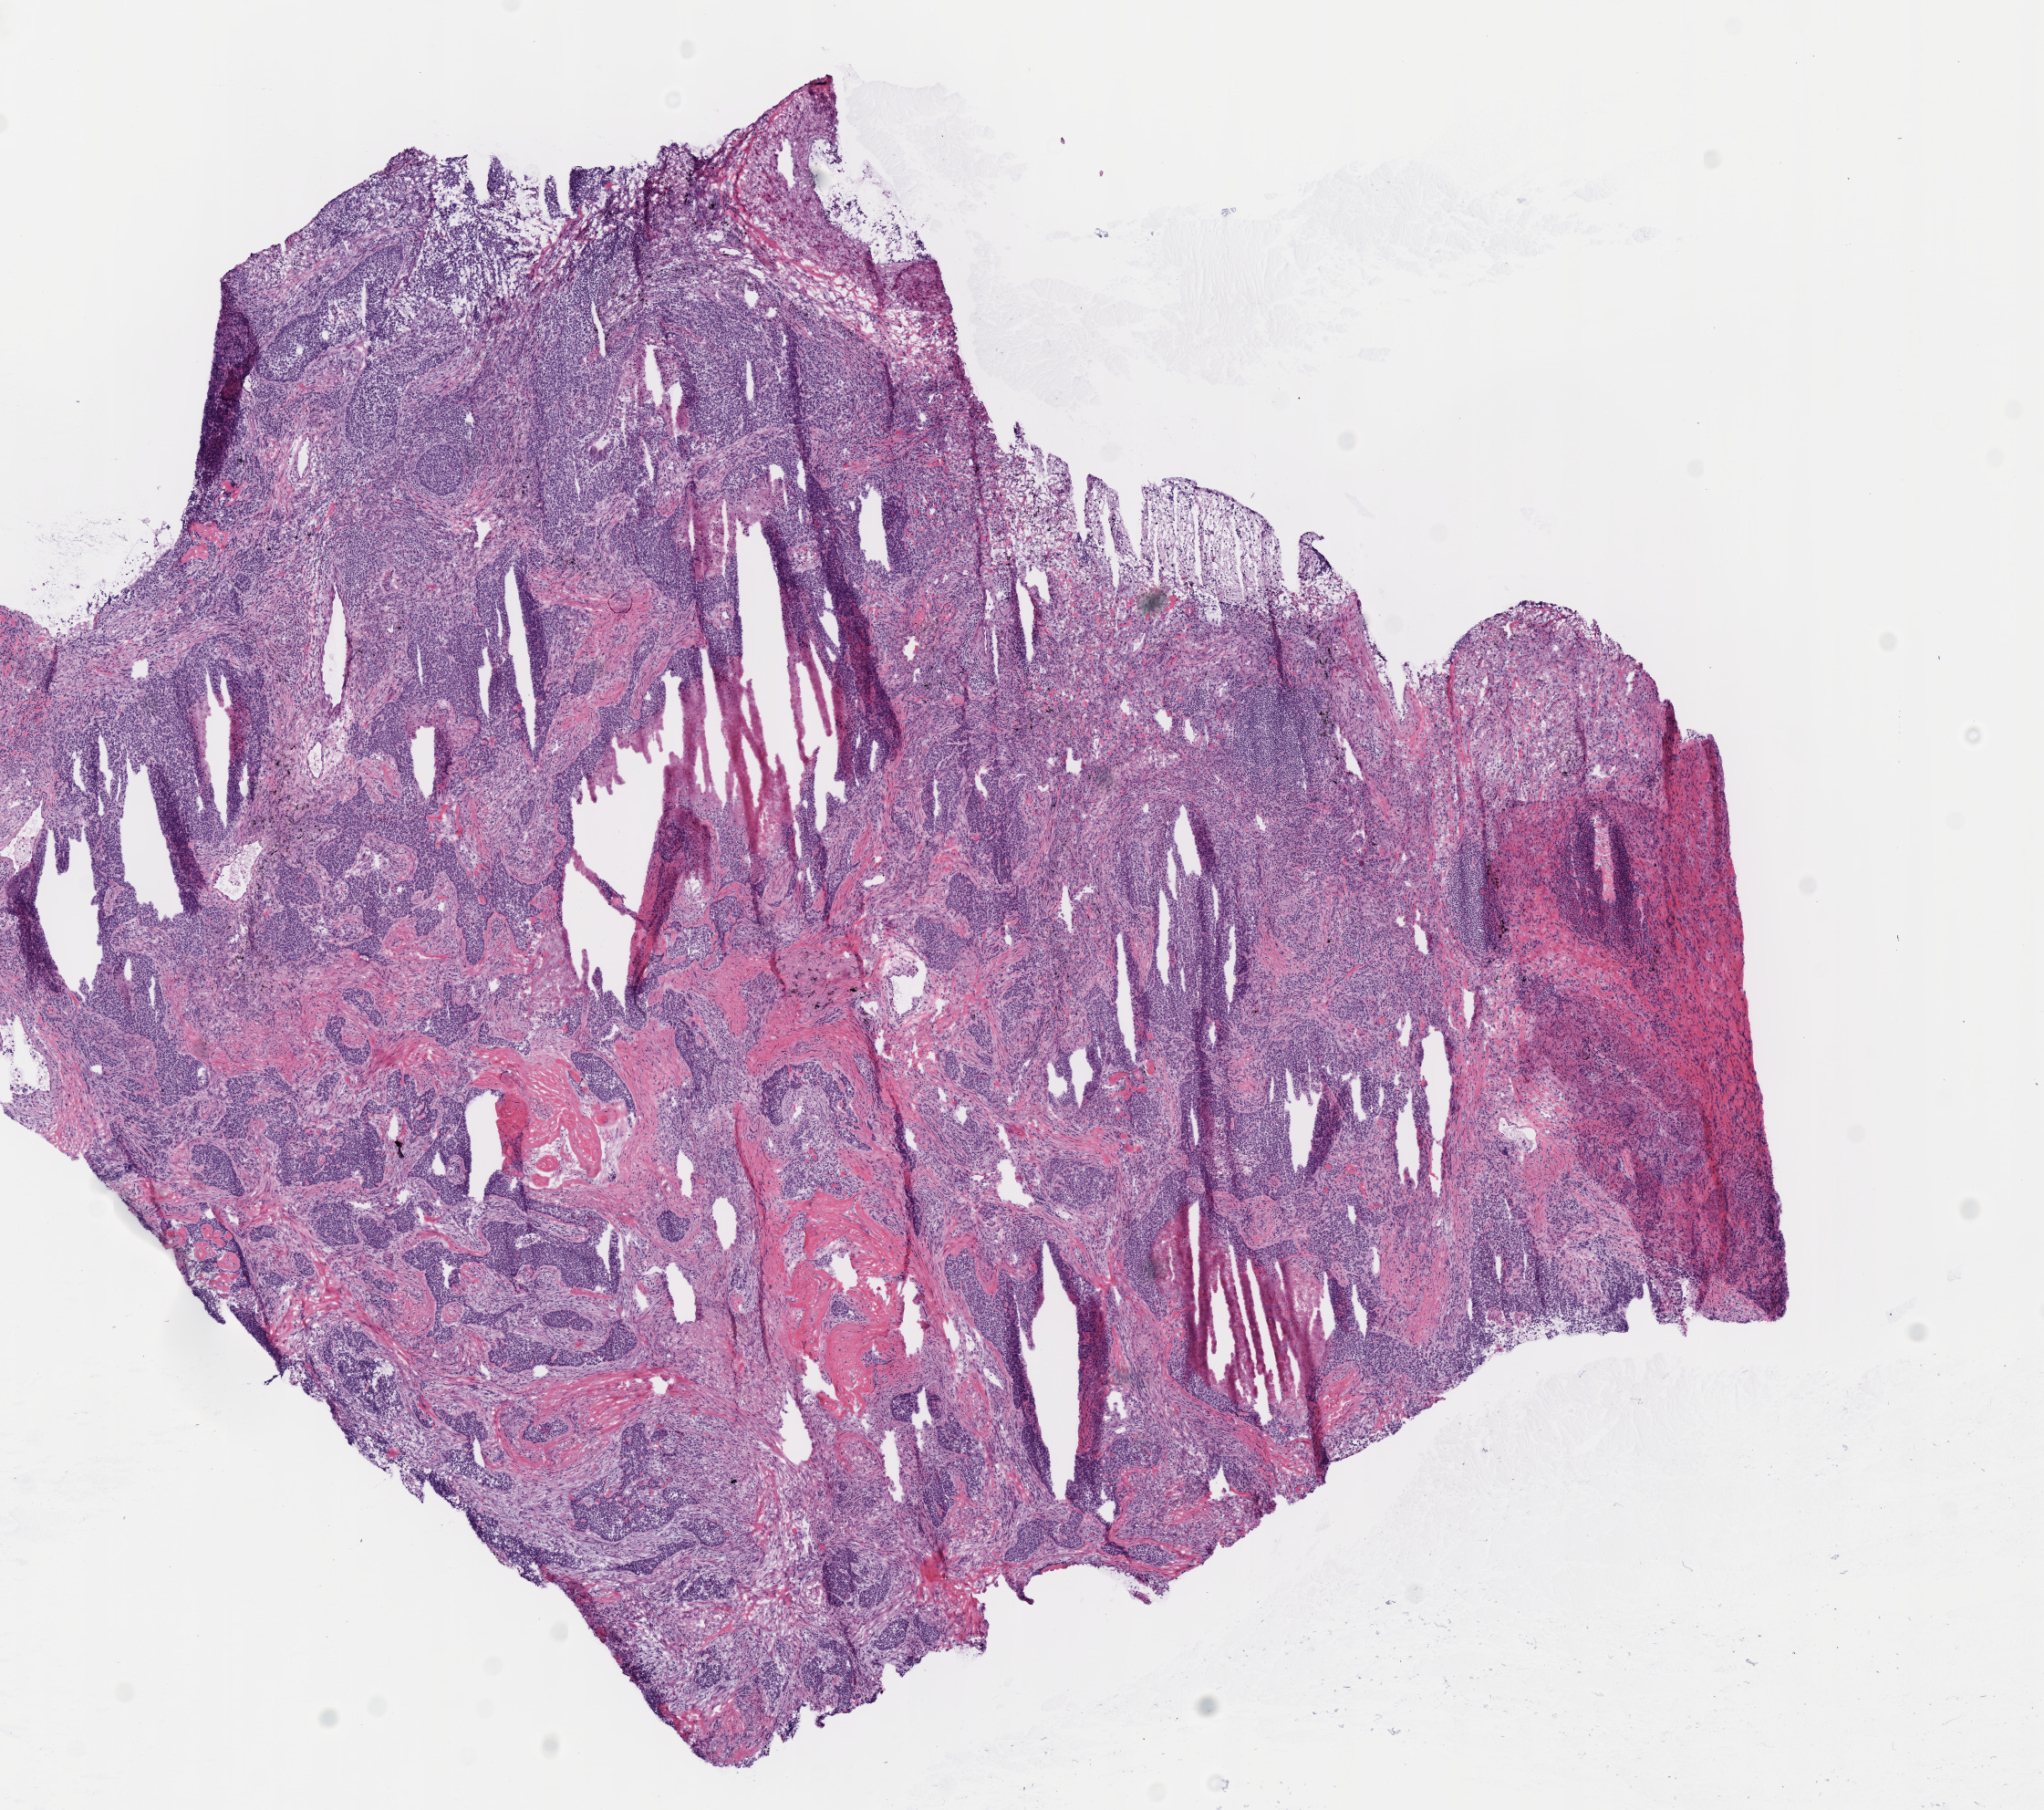
Digitized H&E-stained tissue section (whole slide), a low-resolution overview of the entire scanned area, about 8.8 x 7.8 mm (acquisition: 40x scan); frozen section from the top of the tissue portion; lung, primary tumour sample. Patient: male, age at initial diagnosis 71 years. Pathologist review of this section (percent, as recorded): tumour cells 65%, tumour nuclei 60%, normal cells 0%, stromal cells 25%, necrosis 10%.
Pathologic diagnosis: Squamous cell carcinoma, NOS (lower lobe, lung). AJCC pathologic stage: IA. Laterality: right. TNM: T1b N0 MX.